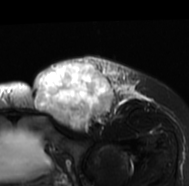
MRI of an extremity soft-tissue mass, one axial slice. Position 49 of 77 along the scan axis. T2-weighted fat-saturated. MR volume resampled by the dataset authors to the PET/CT grid (not the native acquisition matrix). 3.27 mm slice thickness. 189 × 186 image matrix, field of view 185 × 182 mm. Female patient. From the clinical record (not read from this slice): histological type: leiomyosarcoma; grade: high; site of the primary tumour: groin.
Outlined on this slice (expert contour drawn on MRI and transferred to this co-registered scan by the dataset authors):
- gross tumour volume including surrounding oedema: bounding box [x1, y1, x2, y2] px = [31, 56, 148, 133]
- gross tumour volume (mass): [33, 59, 114, 130]